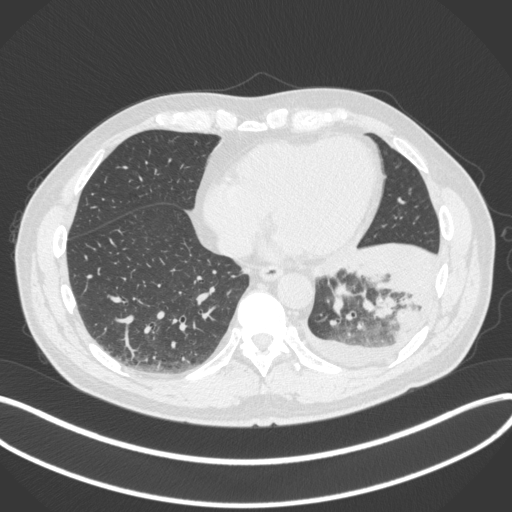
Chest CT, one axial slice; slice 108 of 350 in the series (ordered by position); reconstruction kernel B31f; 120 kVp; lung window (W 1500 / L -600 HU); 1 mm slice thickness; 512 × 512 image matrix. Male patient, age 58 years. From the clinical record (not read from this slice): clinical TNM (as recorded): T3 N1 M1b; histopathological grade: G3.
Outlined on this slice (bounding box drawn by a radiologist):
- lung tumour (recorded histology: small cell carcinoma): box from (x=327, y=279) to (x=352, y=323) px